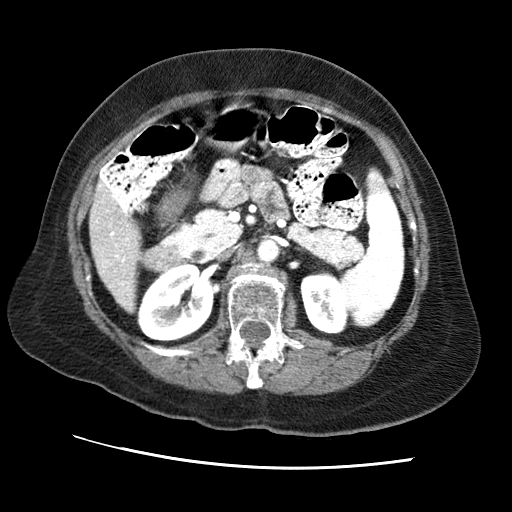
Contrast-enhanced abdominal CT (liver protocol), one axial slice. Reconstruction kernel STANDARD. Soft-tissue window (W 400 / L 40 HU). 2.5 mm slice thickness. 512 × 512 image matrix. From the clinical record (not read from this slice): diagnosis: hepatocellular carcinoma (patient treated with transarterial chemoembolisation; whether this scan precedes or follows treatment is not stated here); TNM stage (as recorded): Stage-II; Child-Pugh class: A; tumour differentiation: no biopsy; tumour nodularity: multinodular.
Structures marked on this image (semi-automatic segmentation, software-assisted and operator-edited):
- liver parenchyma outside the tumour (the mass and vessels are separate outlines, so this box may not span the whole liver): box from (x=90, y=186) to (x=140, y=310) px
- liver vessels: (x=95, y=201)–(x=130, y=291)